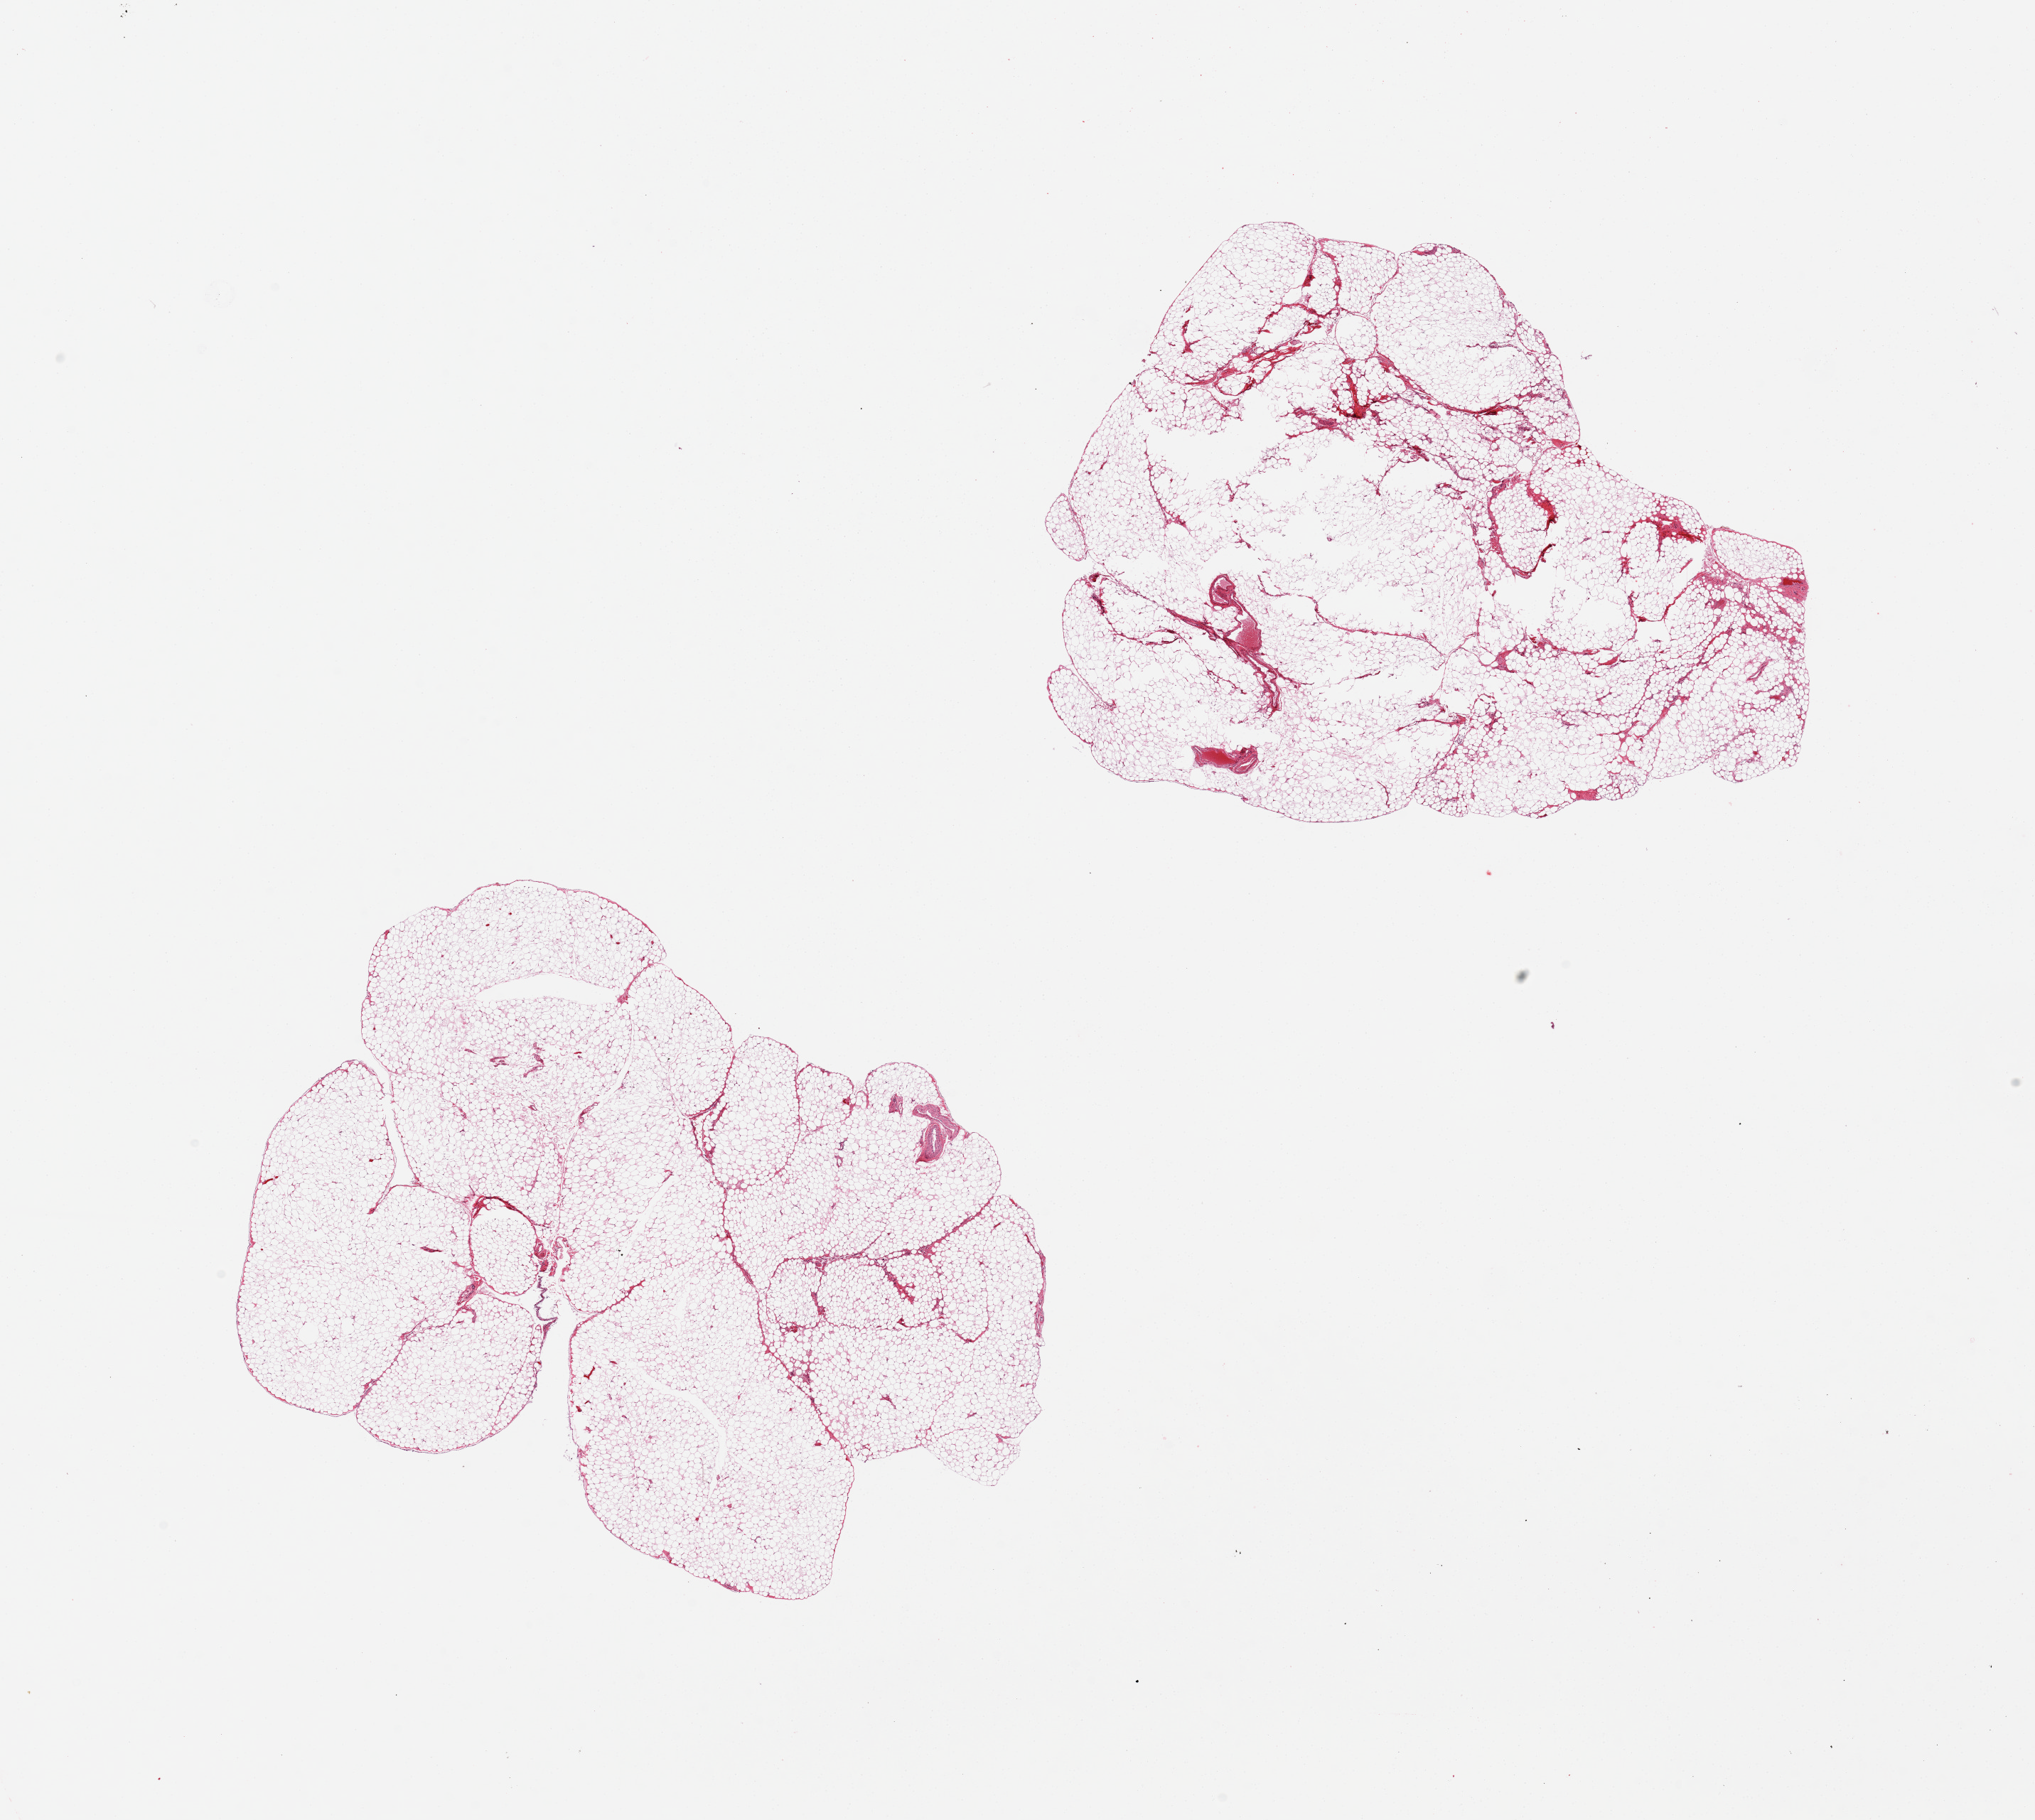
H&E whole-slide image — a low-resolution overview of the entire scanned area, about 22.6 x 20.3 mm (slide scanned at 20x). PAXgene-fixed, paraffin-embedded tissue. Sampled site (target tissue): omentum. Donor tissue sample. Donor: male.
Review note (as recorded): 2 pieces, central defects in 1 piece (?poor fixation).